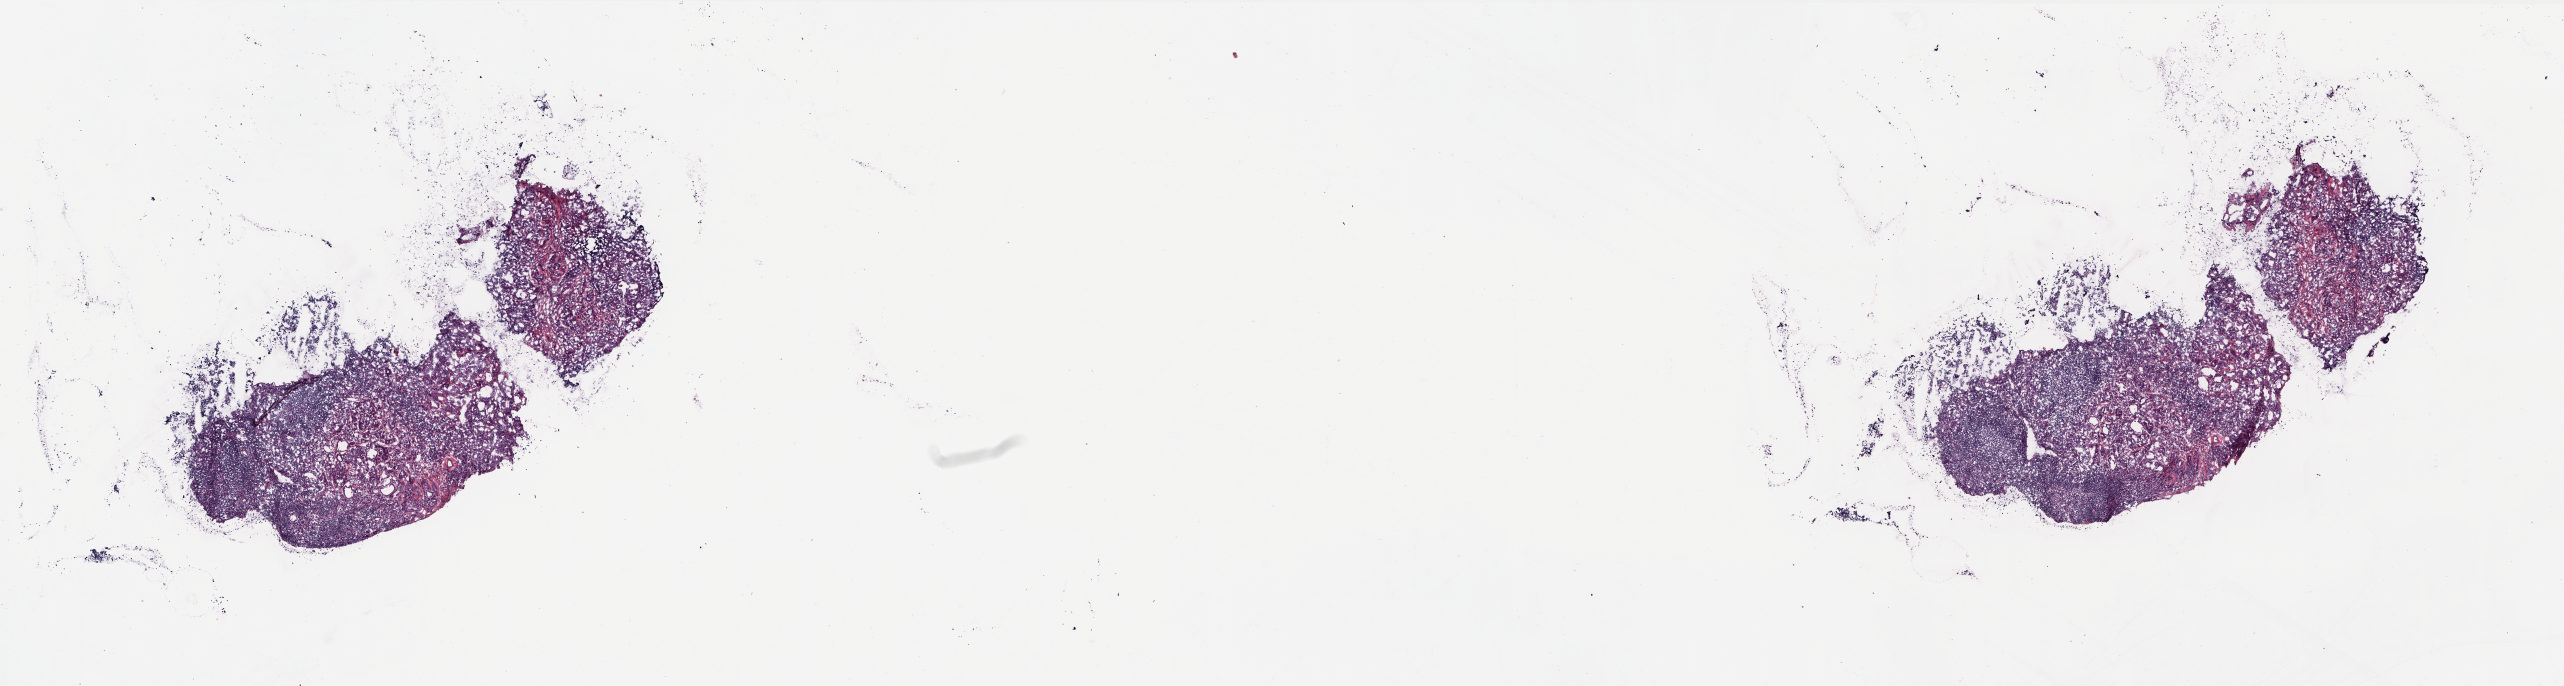
Whole-slide histology image, H&E, a low-resolution overview of the entire scanned area, about 20.7 x 5.5 mm (slide scanned at 20x), frozen section from the top of the tissue portion, thyroid, solid tissue normal (non-tumour tissue) sample. Patient: female, age at initial diagnosis 31 years. Composition of this section per pathologist review: tumour cells 0%, tumour nuclei 0%, normal cells 100%, stromal cells 0%, necrosis 0%. Infiltration values recorded for this section: lymphocyte infiltration 15%, monocyte infiltration 2%, neutrophil infiltration 0%.
This section: solid tissue normal (non-tumour) sample from the same patient. Patient diagnosis: Papillary adenocarcinoma, NOS (thyroid gland).